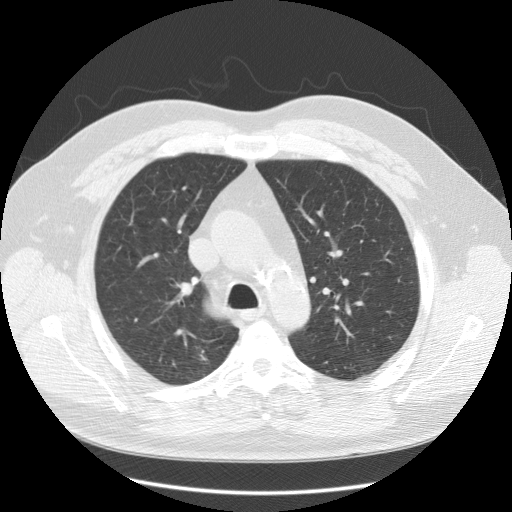
Low-dose screening chest CT, one axial slice; slice 89 of 125 in the series (ordered by position); 120 kVp; lung window (W 1500 / L -600 HU); 512 × 512 image matrix, field of view 380 × 380 mm.
Structures marked on this image (manually delineated by an expert):
- lesion 1 (tumor, upper lobe of right lung): bounding box [x1, y1, x2, y2] px = [200, 350, 207, 360]